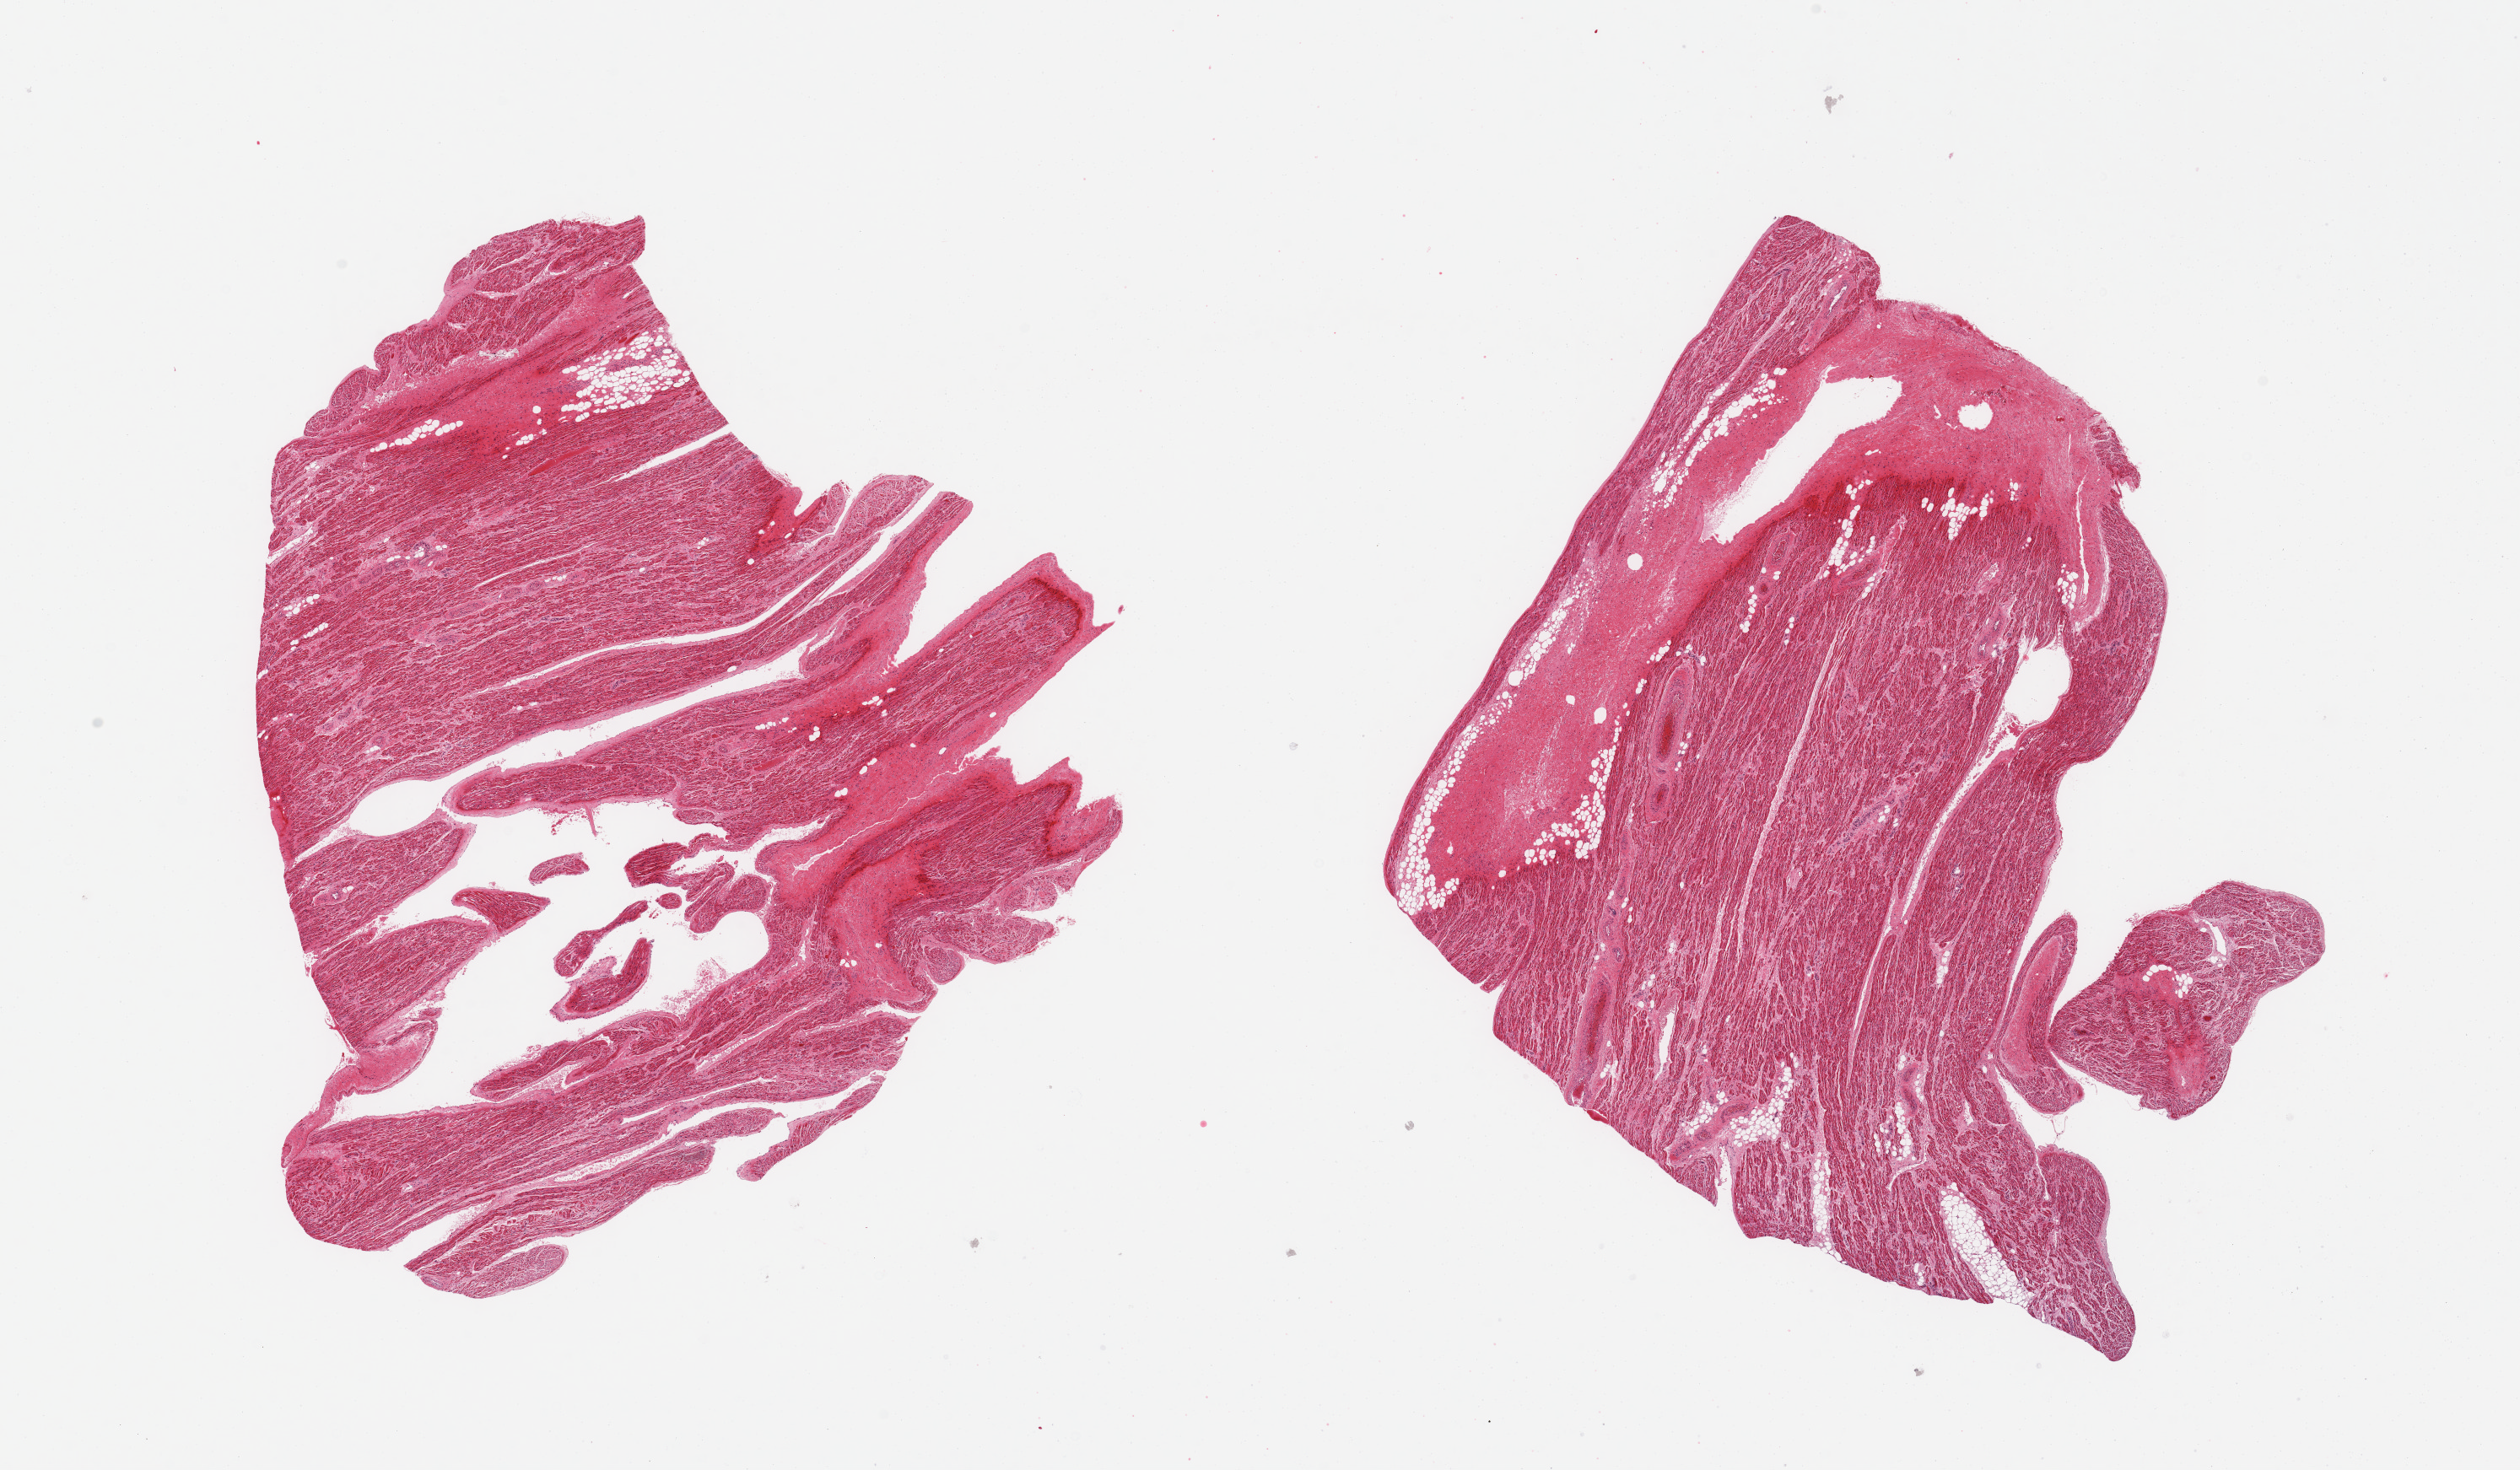
Digitized haematoxylin and eosin-stained section, low-resolution overview of the scanned area, about 23.6 x 13.8 mm (from a 20x scan); PAXgene-fixed, paraffin-embedded tissue; target tissue: auricular appendage; tissue donor sample.
• review note (as recorded): 2 pieces; from 10-20% fibrous/fat